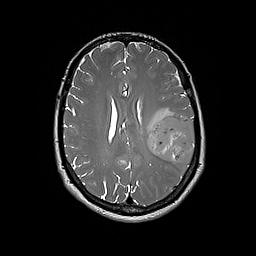
Brain MRI from a brain-tumour surgery series, one axial slice; position 82 of 192 along the scan axis; 1 mm slice thickness; 256 × 256 image matrix, field of view 250 × 250 mm. Case-level facts recorded for this patient, not image findings: histopathology: Glioblastoma; WHO grade: 4.
Structures marked on this image (expert manual segmentation):
- tumour: bounding box [x1, y1, x2, y2] px = [147, 116, 195, 165]